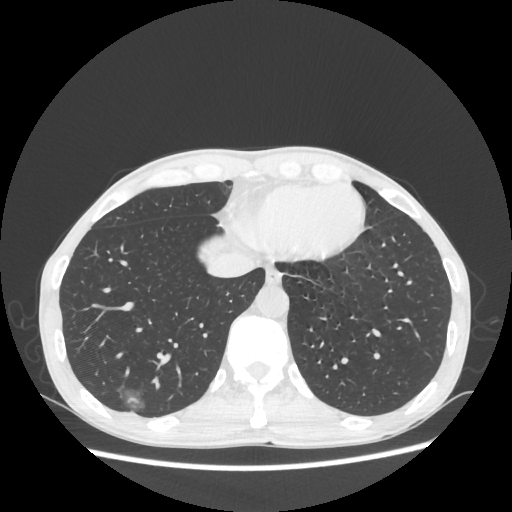
Chest CT, one axial slice; 100 kVp; lung window (W 1500 / L -600 HU); 512 × 512 image matrix. Male patient, age 60 years. Case-level facts recorded for this patient, not image findings: clinical TNM (as recorded): T1c N0 M0.
Annotated regions visible in this slice (rectangle marked by the reading radiologist):
- lung tumour (recorded histology: adenocarcinoma): box from (x=117, y=381) to (x=149, y=410) px